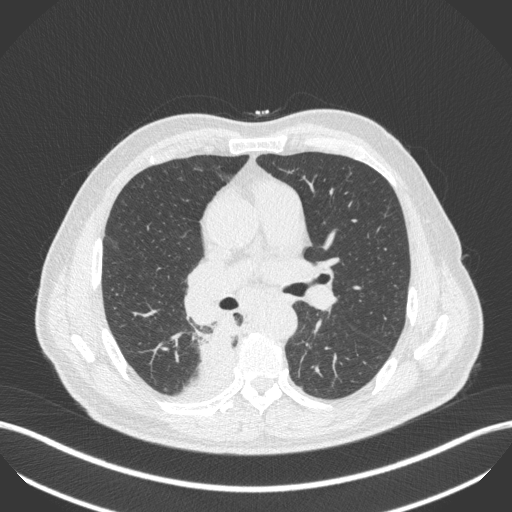
Chest CT, one axial slice; position 268 of 451 along the scan axis; lung window (W 1500 / L -600 HU); 1 mm slice thickness; 512 × 512 image matrix, field of view 400 × 400 mm. Patient: male, 61 years. Case-level facts recorded for this patient, not image findings: clinical TNM (as recorded): T1 N0 M0.
Outlined on this slice (rectangle marked by the reading radiologist):
- lung tumour (recorded histology: small cell carcinoma): box from (x=194, y=316) to (x=240, y=366) px